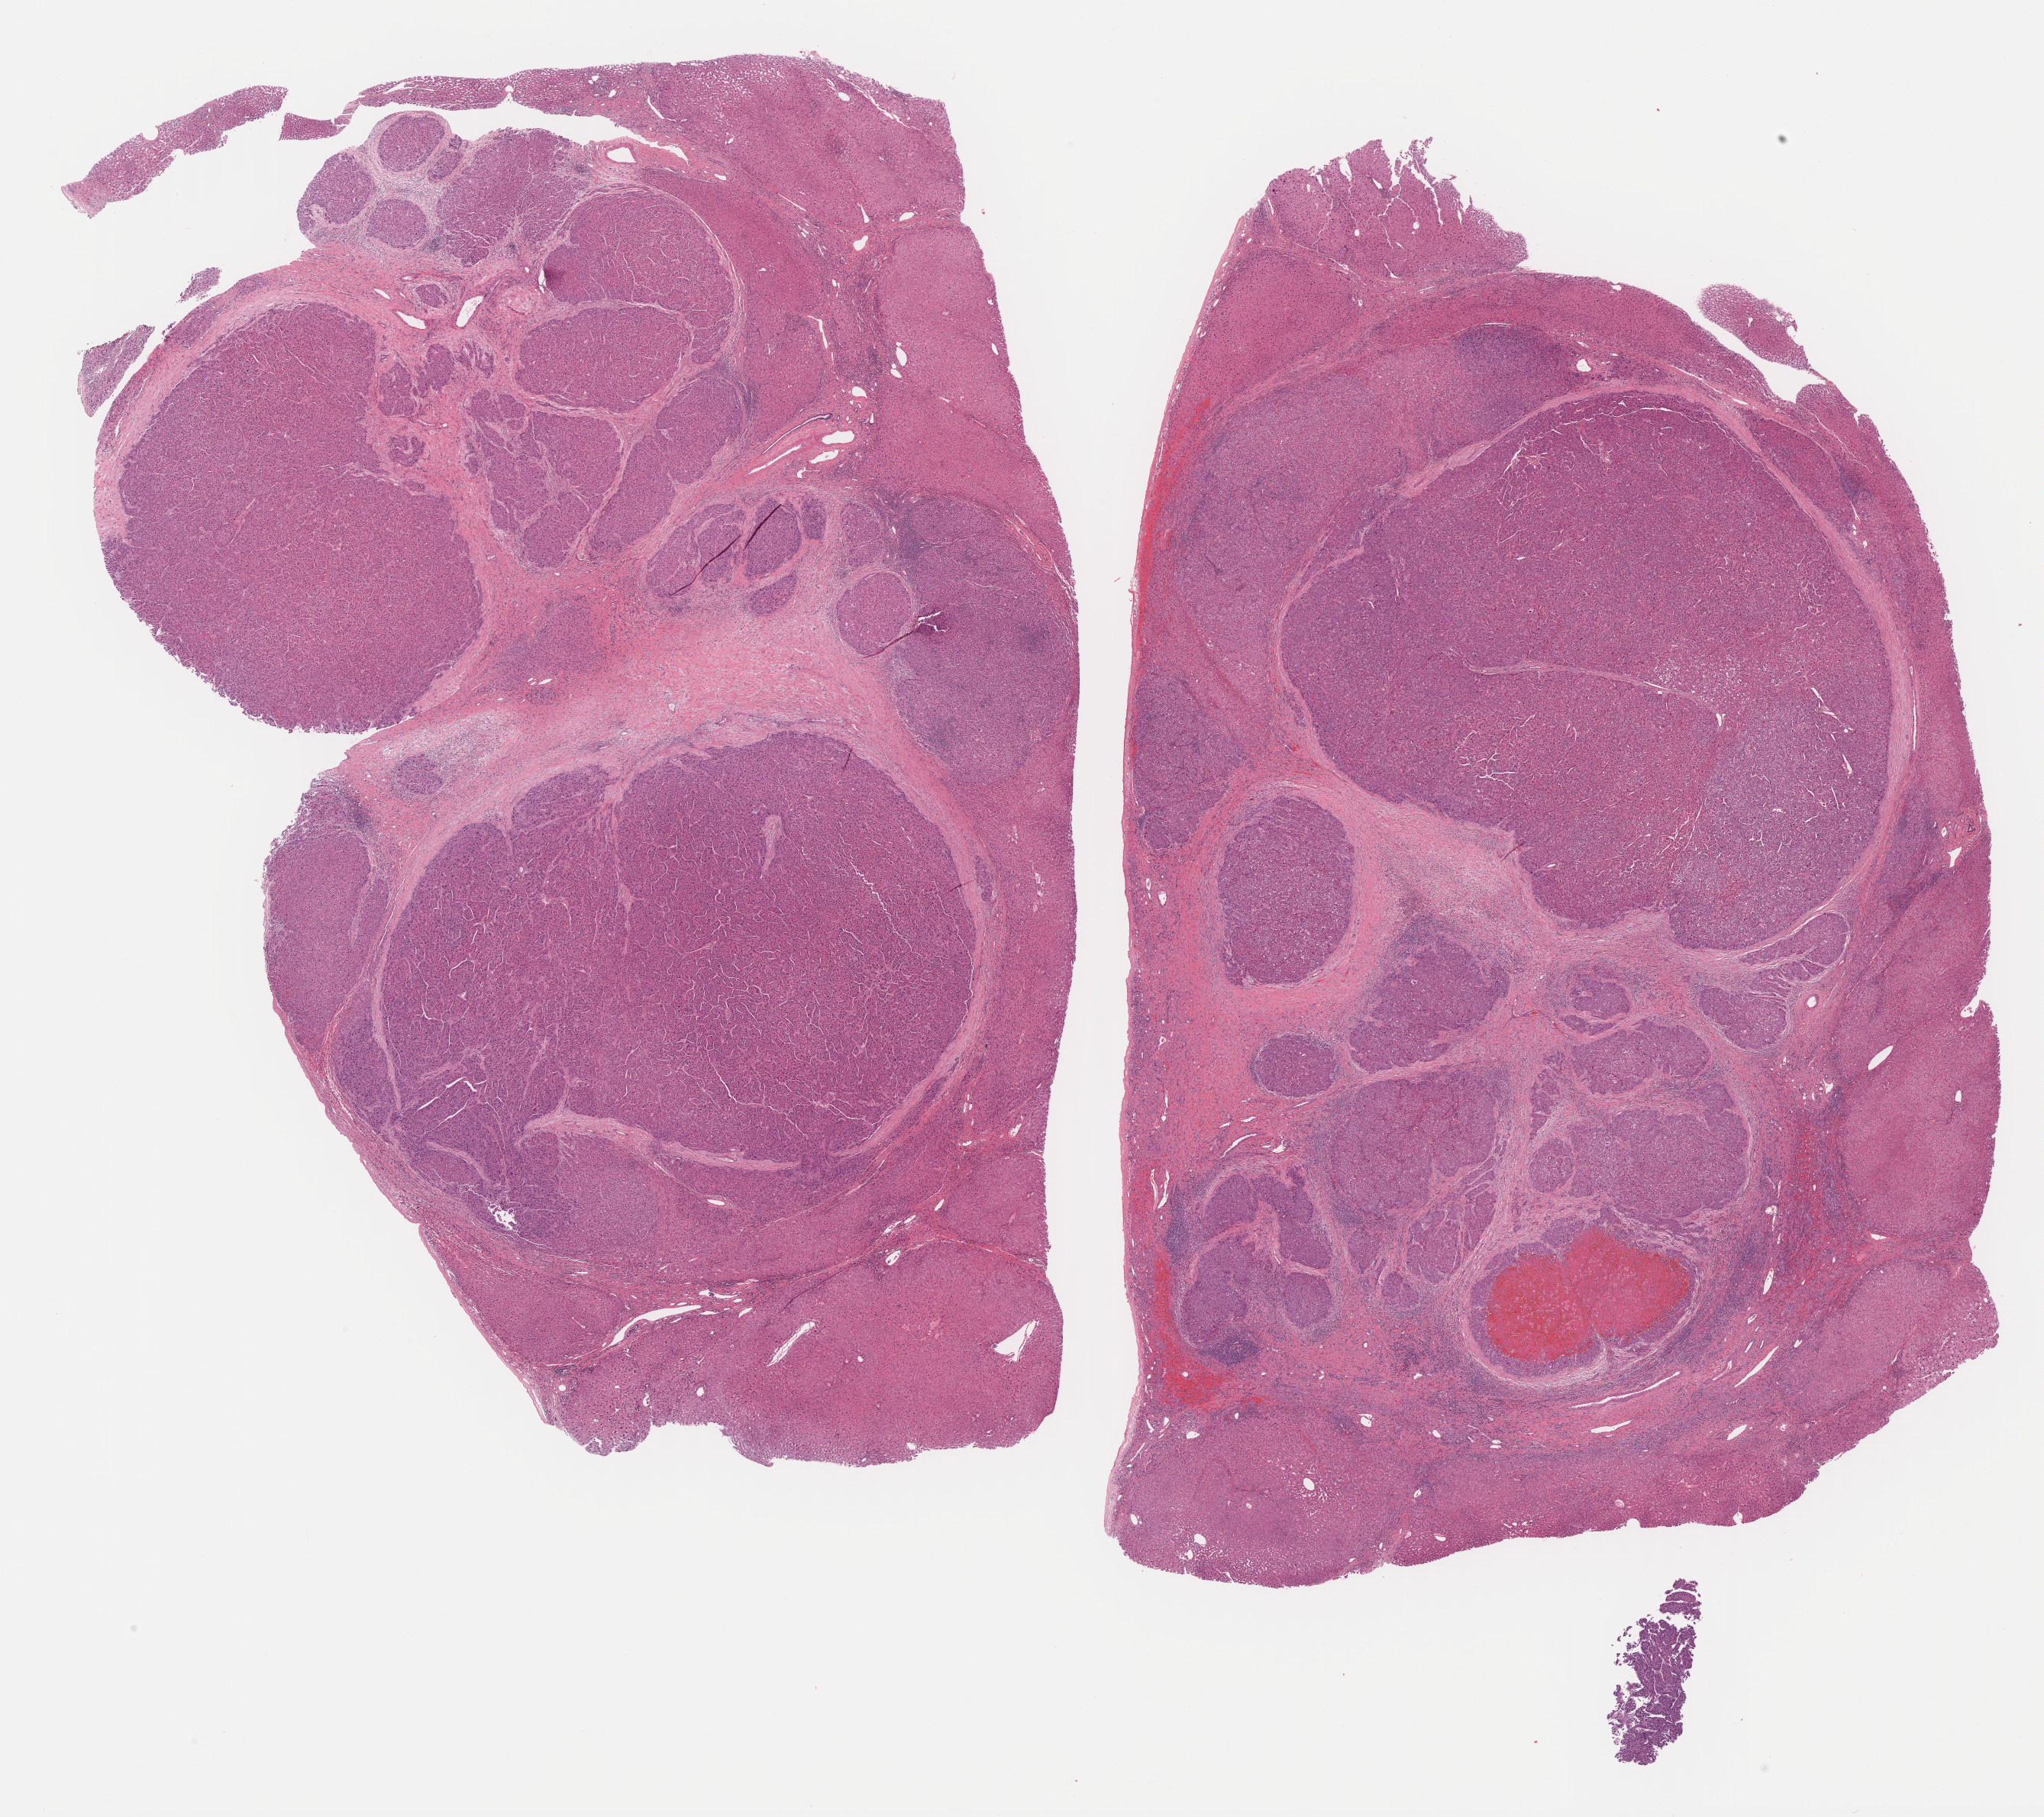
Whole-slide histology image, Hematoxylin and eosin (H&E) stained, shown as a low-resolution overview of the whole scanned area (about 21.7 x 19.3 mm, slide scanned at 40x); formalin-fixed paraffin-embedded (FFPE) diagnostic section; liver, primary tumour sample. Patient: male, age at initial diagnosis 23 years. Histologic grade: G3 (poorly differentiated).
AJCC pathologic stage: II (6th edition). Diagnosis: Hepatocellular carcinoma, NOS.